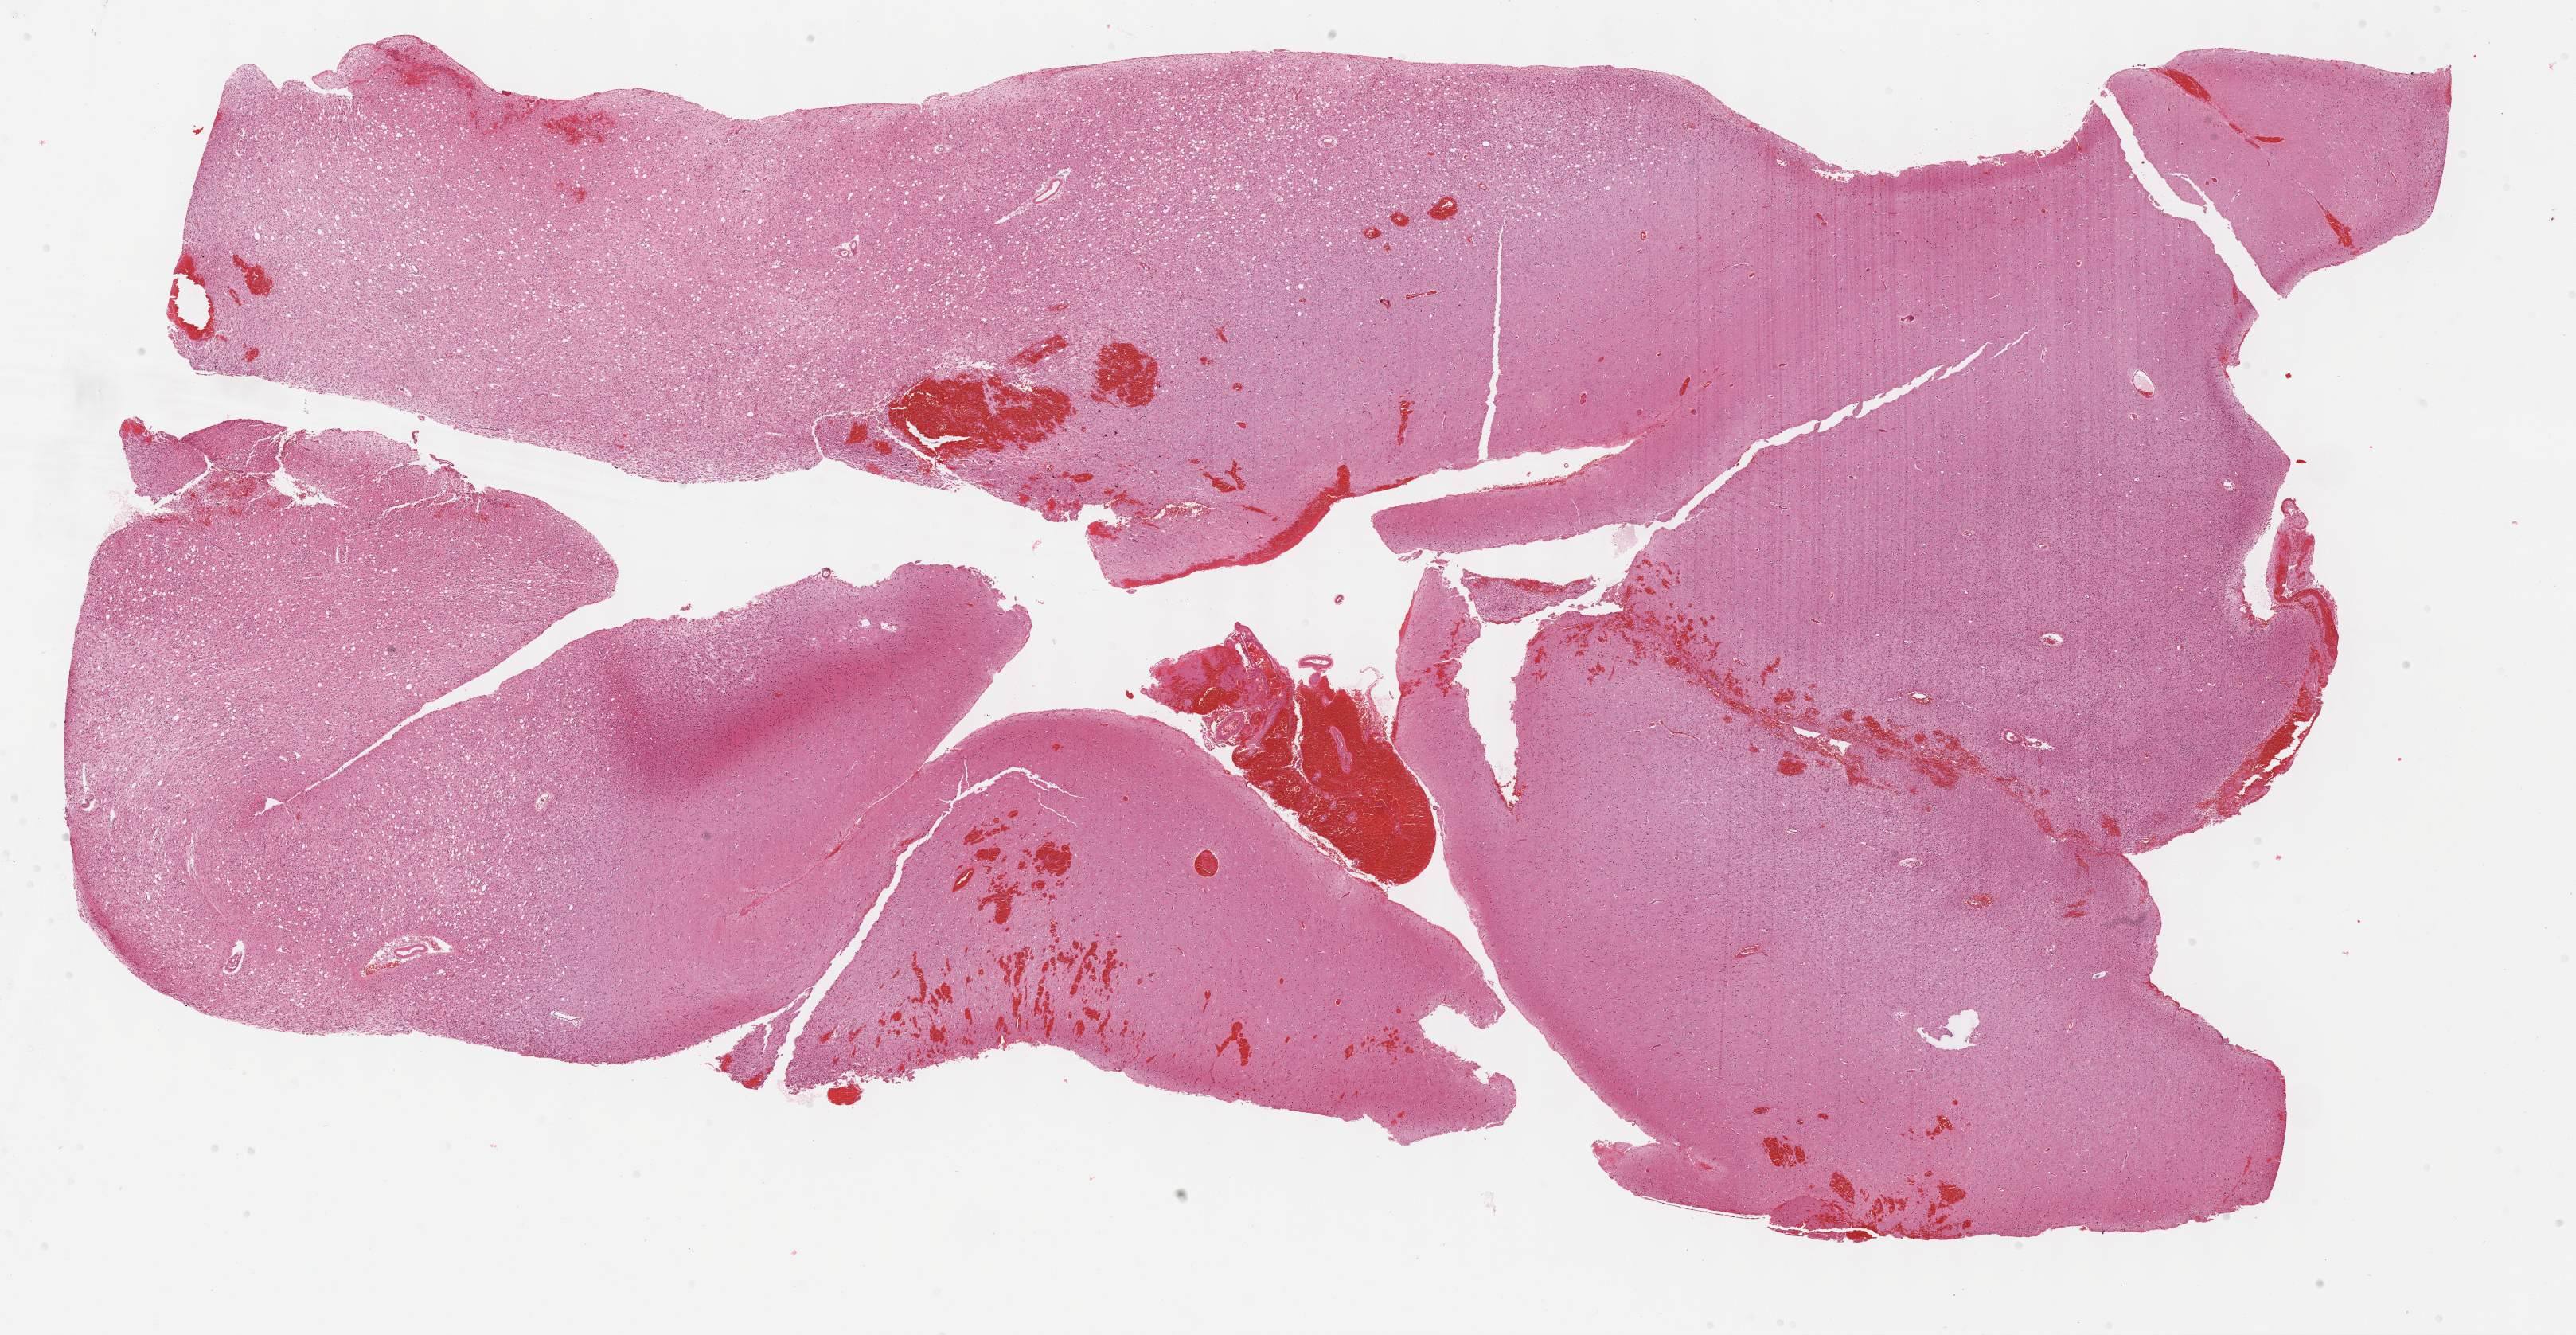
Whole-slide histology image, H&E — low-resolution overview of the scanned area, about 26.2 x 13.6 mm, formalin-fixed paraffin-embedded (FFPE) diagnostic section, sample: primary tumour, brain. Patient: male, age at initial diagnosis 30 years. Histologic grade: G3 (poorly differentiated).
Histologic diagnosis: Astrocytoma, anaplastic (cerebrum). Laterality: left.